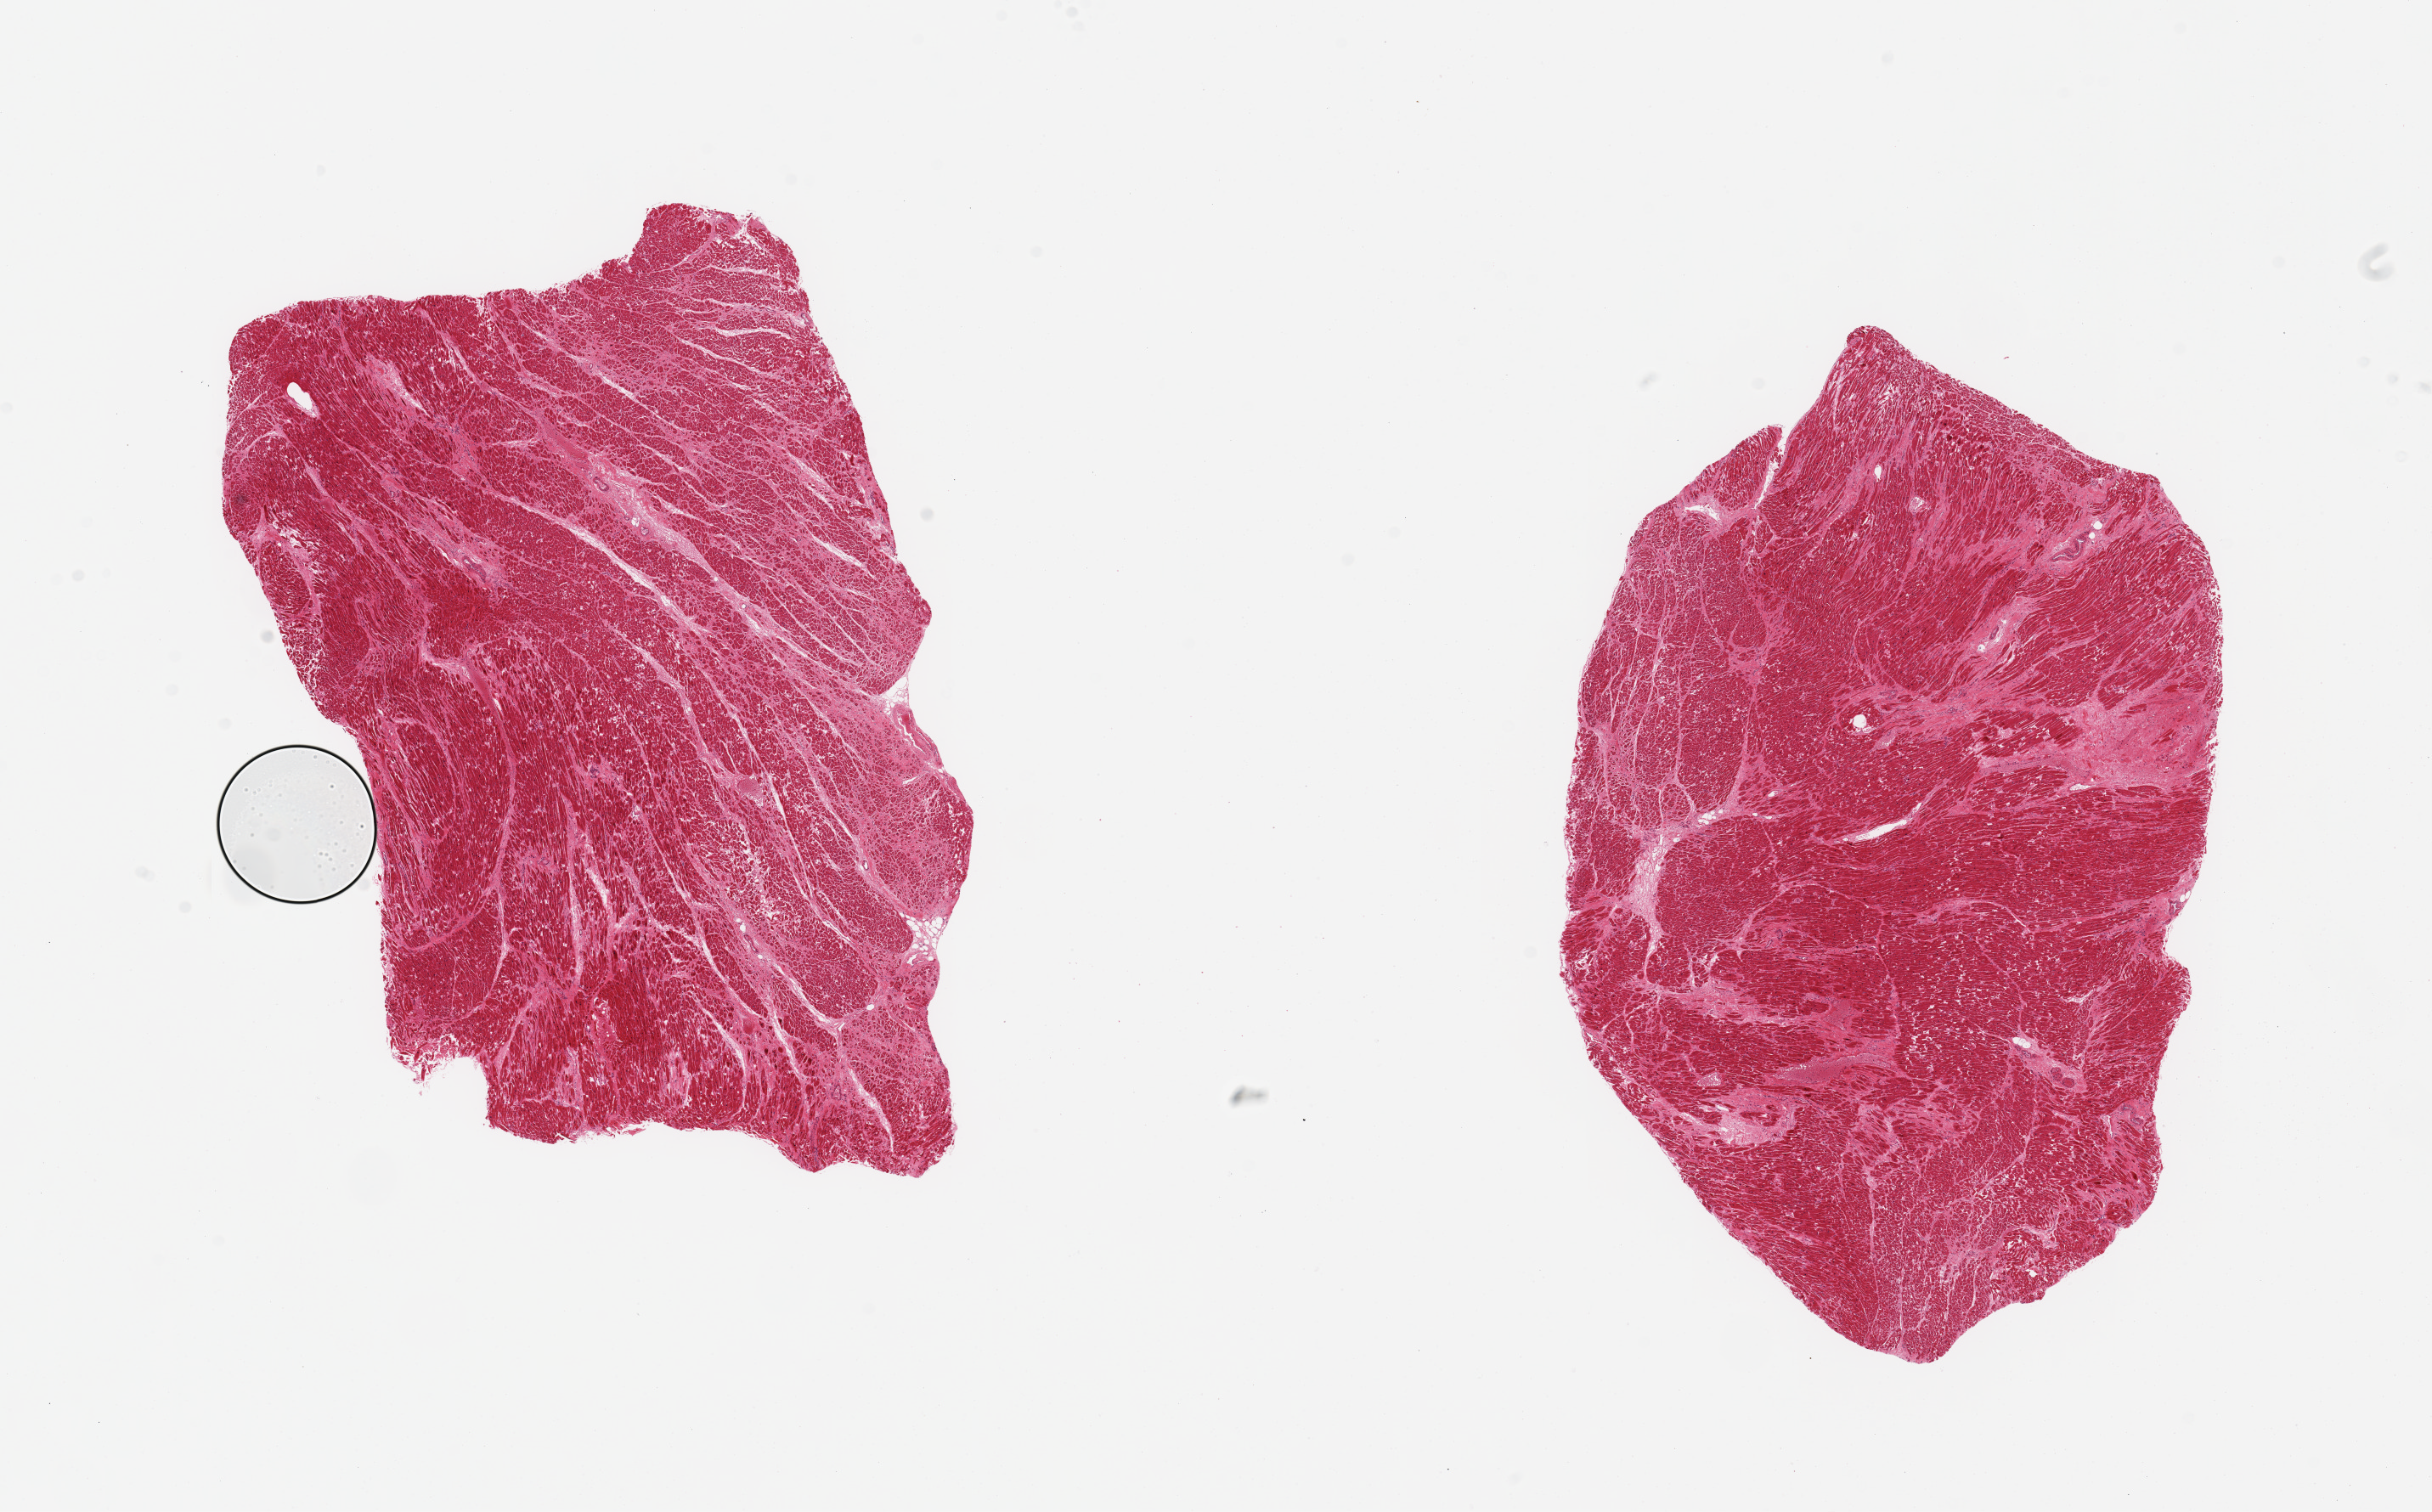
Digitized H&E-stained section — shown as a low-resolution overview of the whole scanned area (about 22.6 x 14.1 mm, slide scanned at 20x); PAXgene-fixed, paraffin-embedded tissue; target tissue: heart; tissue donor sample. Donor: male.
* reviewer comment on this tissue sample: 2 pieces; extensive interstitial fibrosis with scarring